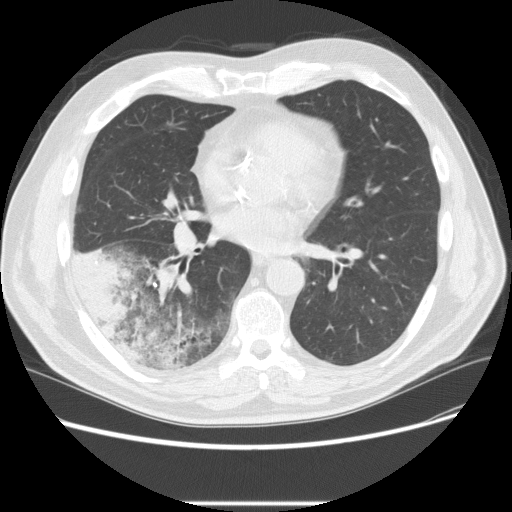
Low-dose screening chest CT, one axial slice. Position 104 of 233 along the scan axis. Reconstruction kernel STANDARD. 120 kVp. Lung window (W 1500 / L -600 HU). 2.5 mm slice thickness. 512 × 512 image matrix, field of view 380 × 380 mm.
Annotated regions visible in this slice (expert manual segmentation):
- lesion 3 (tumor, lower lobe of right lung): box from (x=71, y=245) to (x=132, y=327) px